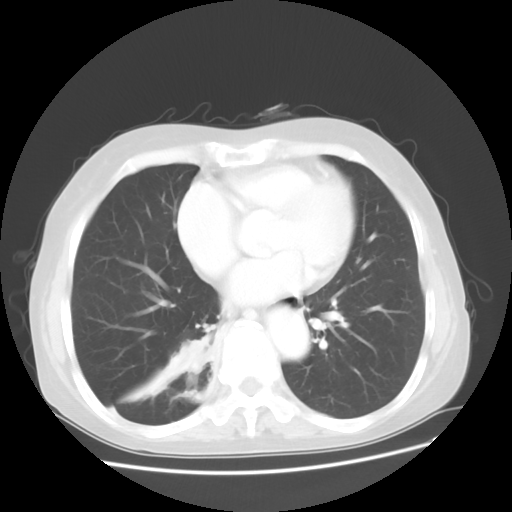
Chest CT, one axial slice; position 16 of 48 along the scan axis; reconstruction kernel STANDARD; lung window (W 1500 / L -600 HU); 5 mm slice thickness; 512 × 512 image matrix. Patient: female, 63 years. Case-level facts recorded for this patient, not image findings: clinical TNM (as recorded): T2 N3 M1b; histopathological grade: G3.
Structures marked on this image (rectangle marked by the reading radiologist):
- lung tumour (recorded histology: small cell carcinoma): box from (x=175, y=327) to (x=213, y=389) px